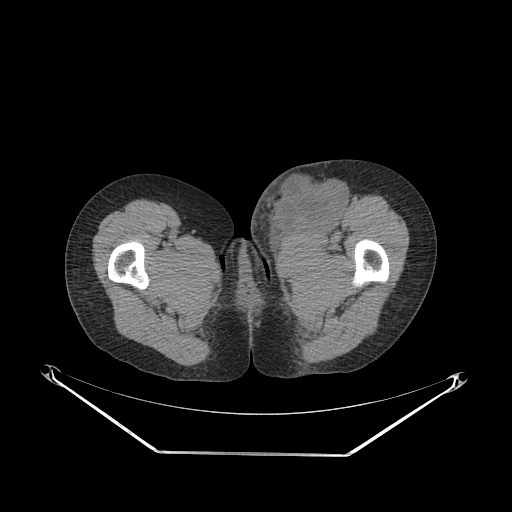
CT of an extremity soft-tissue mass (from a PET/CT study), one axial slice; position 50 of 267 along the scan axis; 140 kVp; soft-tissue window (W 400 / L 40 HU); 512 × 512 image matrix, field of view 500 × 500 mm. Female patient. From the clinical record (not read from this slice): histological type: leiomyosarcoma; grade: high; site of the primary tumour: groin.
Outlined on this slice (expert contour drawn on MRI and transferred to this co-registered scan by the dataset authors):
- gross tumour volume including surrounding oedema: bounding box [x1, y1, x2, y2] px = [249, 164, 348, 243]
- gross tumour volume (mass): [272, 176, 348, 234]